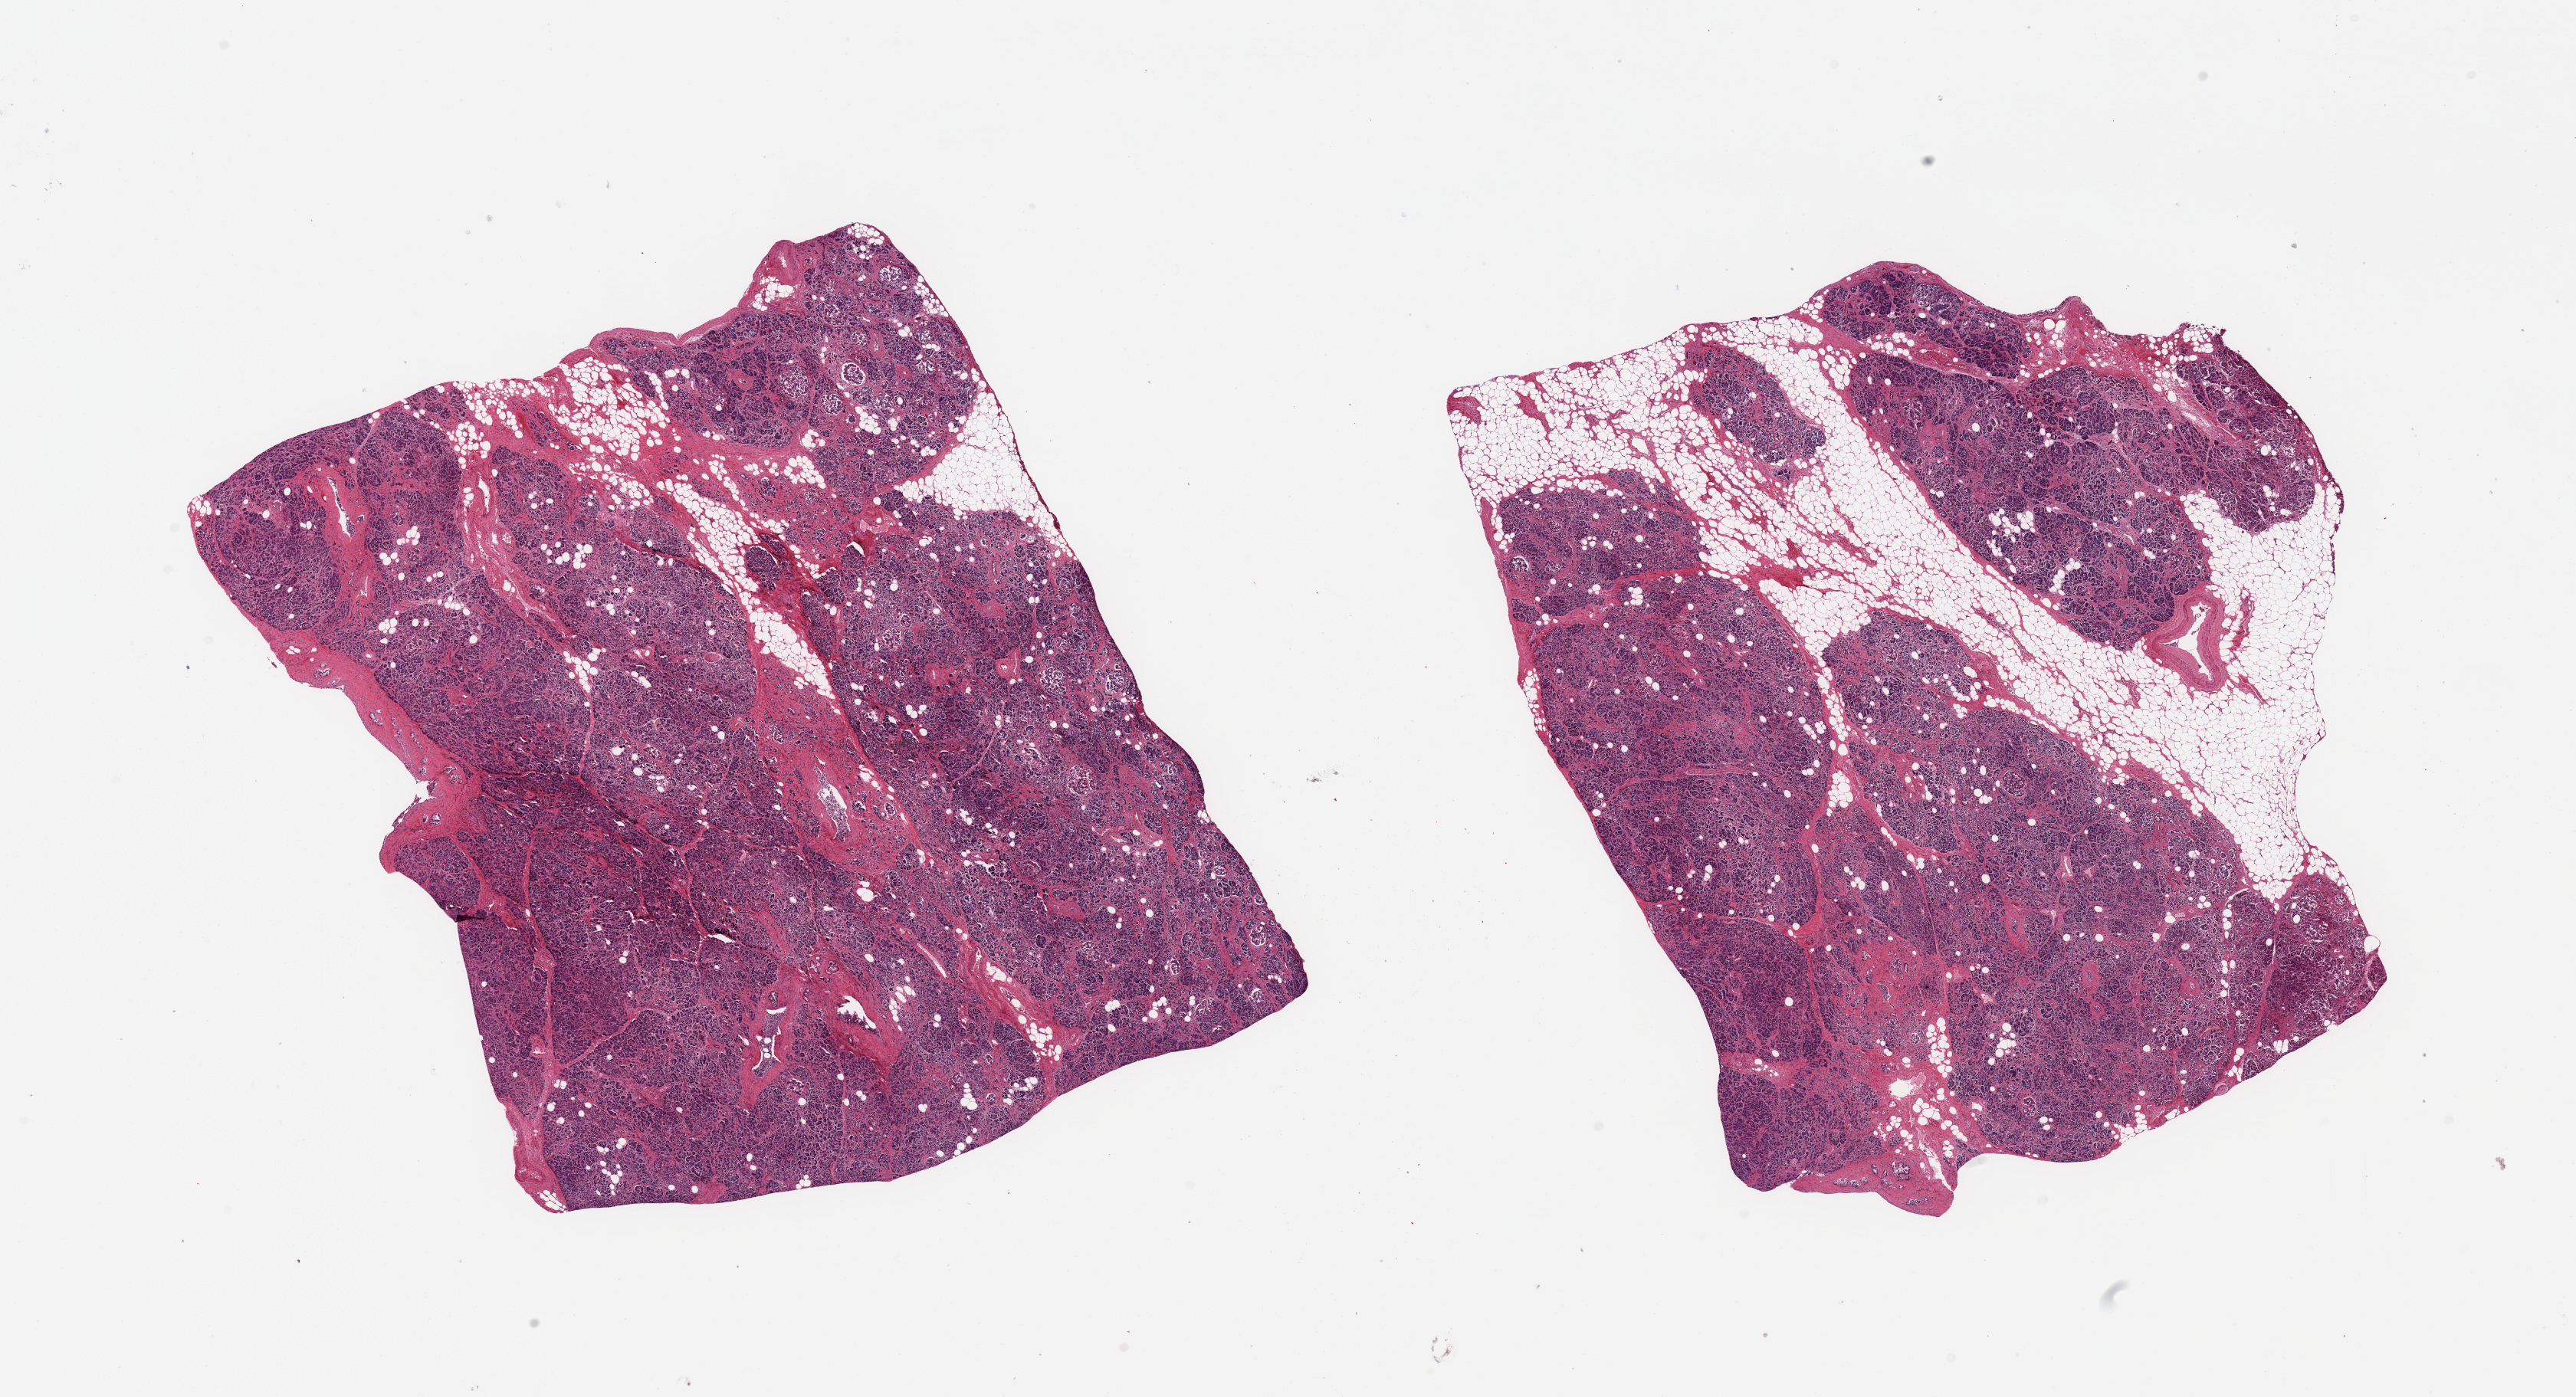
Whole-slide image, H&E stain, a low-resolution overview of the entire scanned area, about 26.6 x 14.4 mm; PAXgene-fixed paraffin-embedded (PFPE) section; section of pancreas (target tissue); tissue donor sample. Male donor.
Reviewer comment on this tissue sample: 2 pieces; 5 & 20% internal fat content; some areas border on severe autolysis.